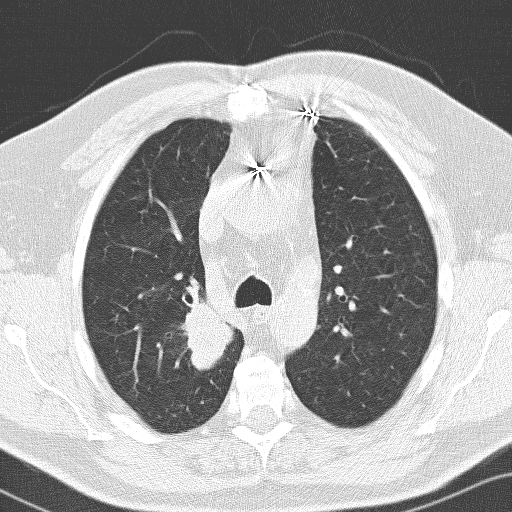
Axial slice from a low-dose chest CT screening exam. First (baseline) screen. Lung window (W 1500 / L -600 HU). 3.2 mm slice thickness. Lung (sharp) reconstruction kernel (D). 512 × 512 image matrix. Male participant, aged 66 years at enrolment. Former smoker at enrolment.
Lesion marked by an expert reader, bounding box <147,298,232,391> (left, top, right, bottom; pixels). Reader record for this screening exam (exam-level; its link to the box is not recorded): non-calcified nodule or mass ≥4 mm, right upper lobe, 36 × 30 mm, spiculated (stellate) margins, soft tissue attenuation.